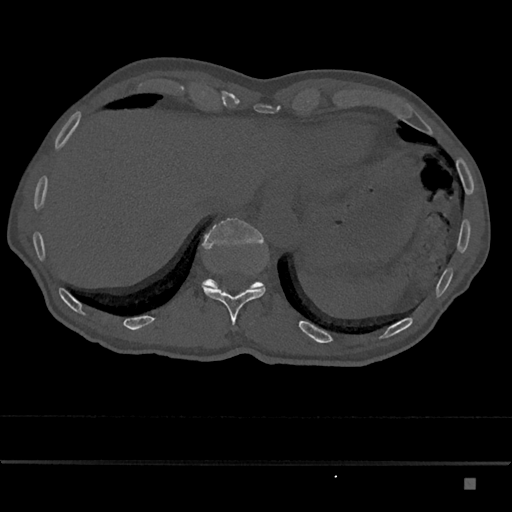
CT including the spine, one axial slice; slice 659 of 797 in the series (ordered by position); reconstruction kernel Br40s/3; bone window (W 1800 / L 400 HU); 0.5 mm slice thickness; 512 × 512 image matrix. Male patient, age 72 years. Case-level facts recorded for this patient, not image findings: primary cancer: prostate.
Structures marked on this image (semi-automatic segmentation, software-assisted and operator-edited):
- T11 vertebra: bounding box <201,283,266,325> (left, top, right, bottom; pixels)
- T12 vertebra: <202,218,265,289>